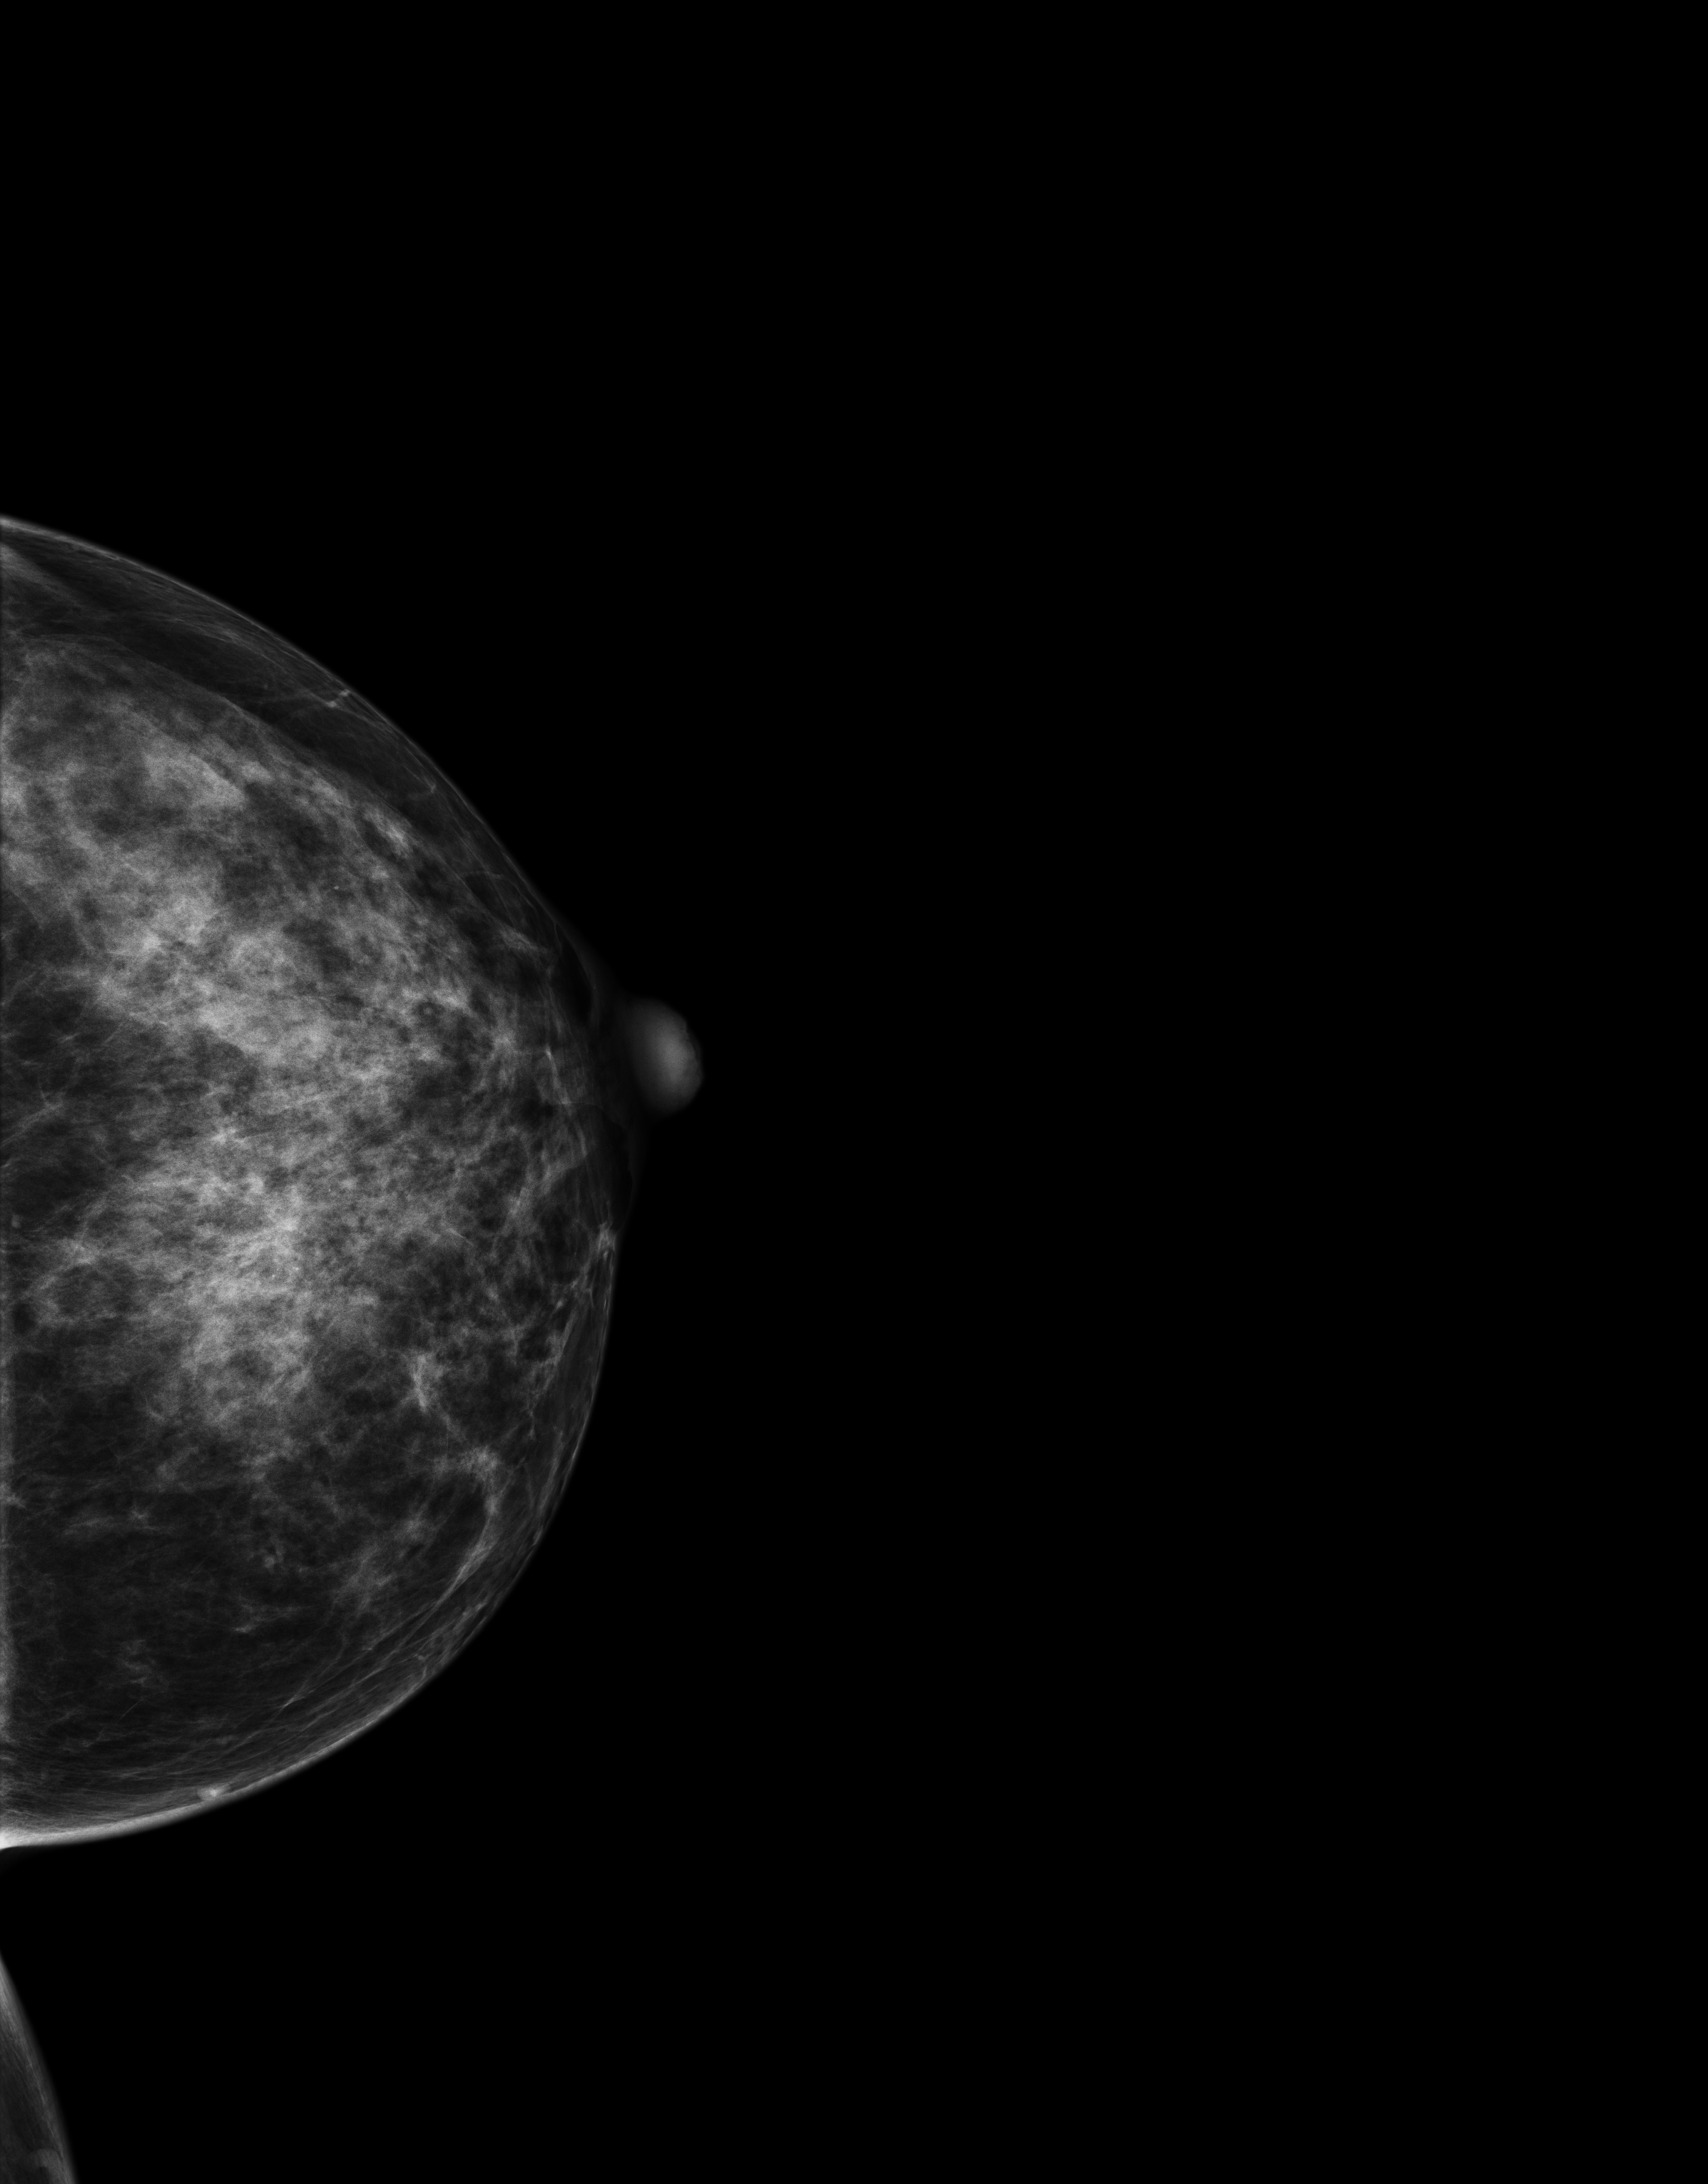
Annual screening mammography examination. Patient aged 43 years (female).
Image type: full-field digital mammogram. Breast: left. Projection: craniocaudal (CC) view.